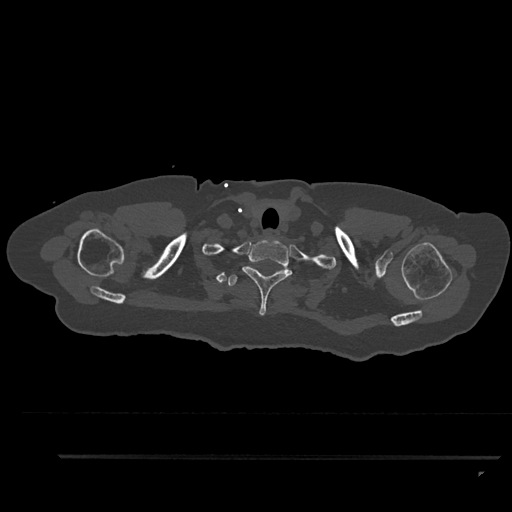
CT including the spine, one axial slice; position 757 of 797 along the scan axis; reconstruction kernel Br40s/3; 120 kVp; bone window (W 1800 / L 400 HU); 0.5 mm slice thickness; 512 × 512 image matrix, field of view 408 × 408 mm. Patient: female, 44 years. From the clinical record (not read from this slice): primary cancer: renal; vertebrae with lytic lesions (as recorded): L1.
Structures marked on this image (semi-automatically segmented with operator editing):
- T1 vertebra: box from (x=242, y=239) to (x=293, y=316) px
- T2 vertebra: (x=228, y=275)–(x=238, y=287)